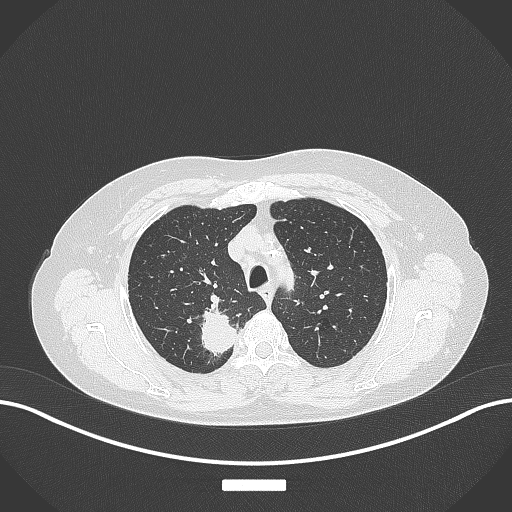
Chest CT, one axial slice. Slice 300 of 357 in the series (ordered by position). 120 kVp. Lung window (W 1500 / L -600 HU). 1 mm slice thickness. 512 × 512 image matrix. Patient: female, 62 years. Case-level facts recorded for this patient, not image findings: clinical TNM (as recorded): T1c N1 M0.
Structures marked on this image (bounding box drawn by a radiologist):
- lung tumour (recorded histology: squamous cell carcinoma): bounding box <192,300,239,359> (left, top, right, bottom; pixels)